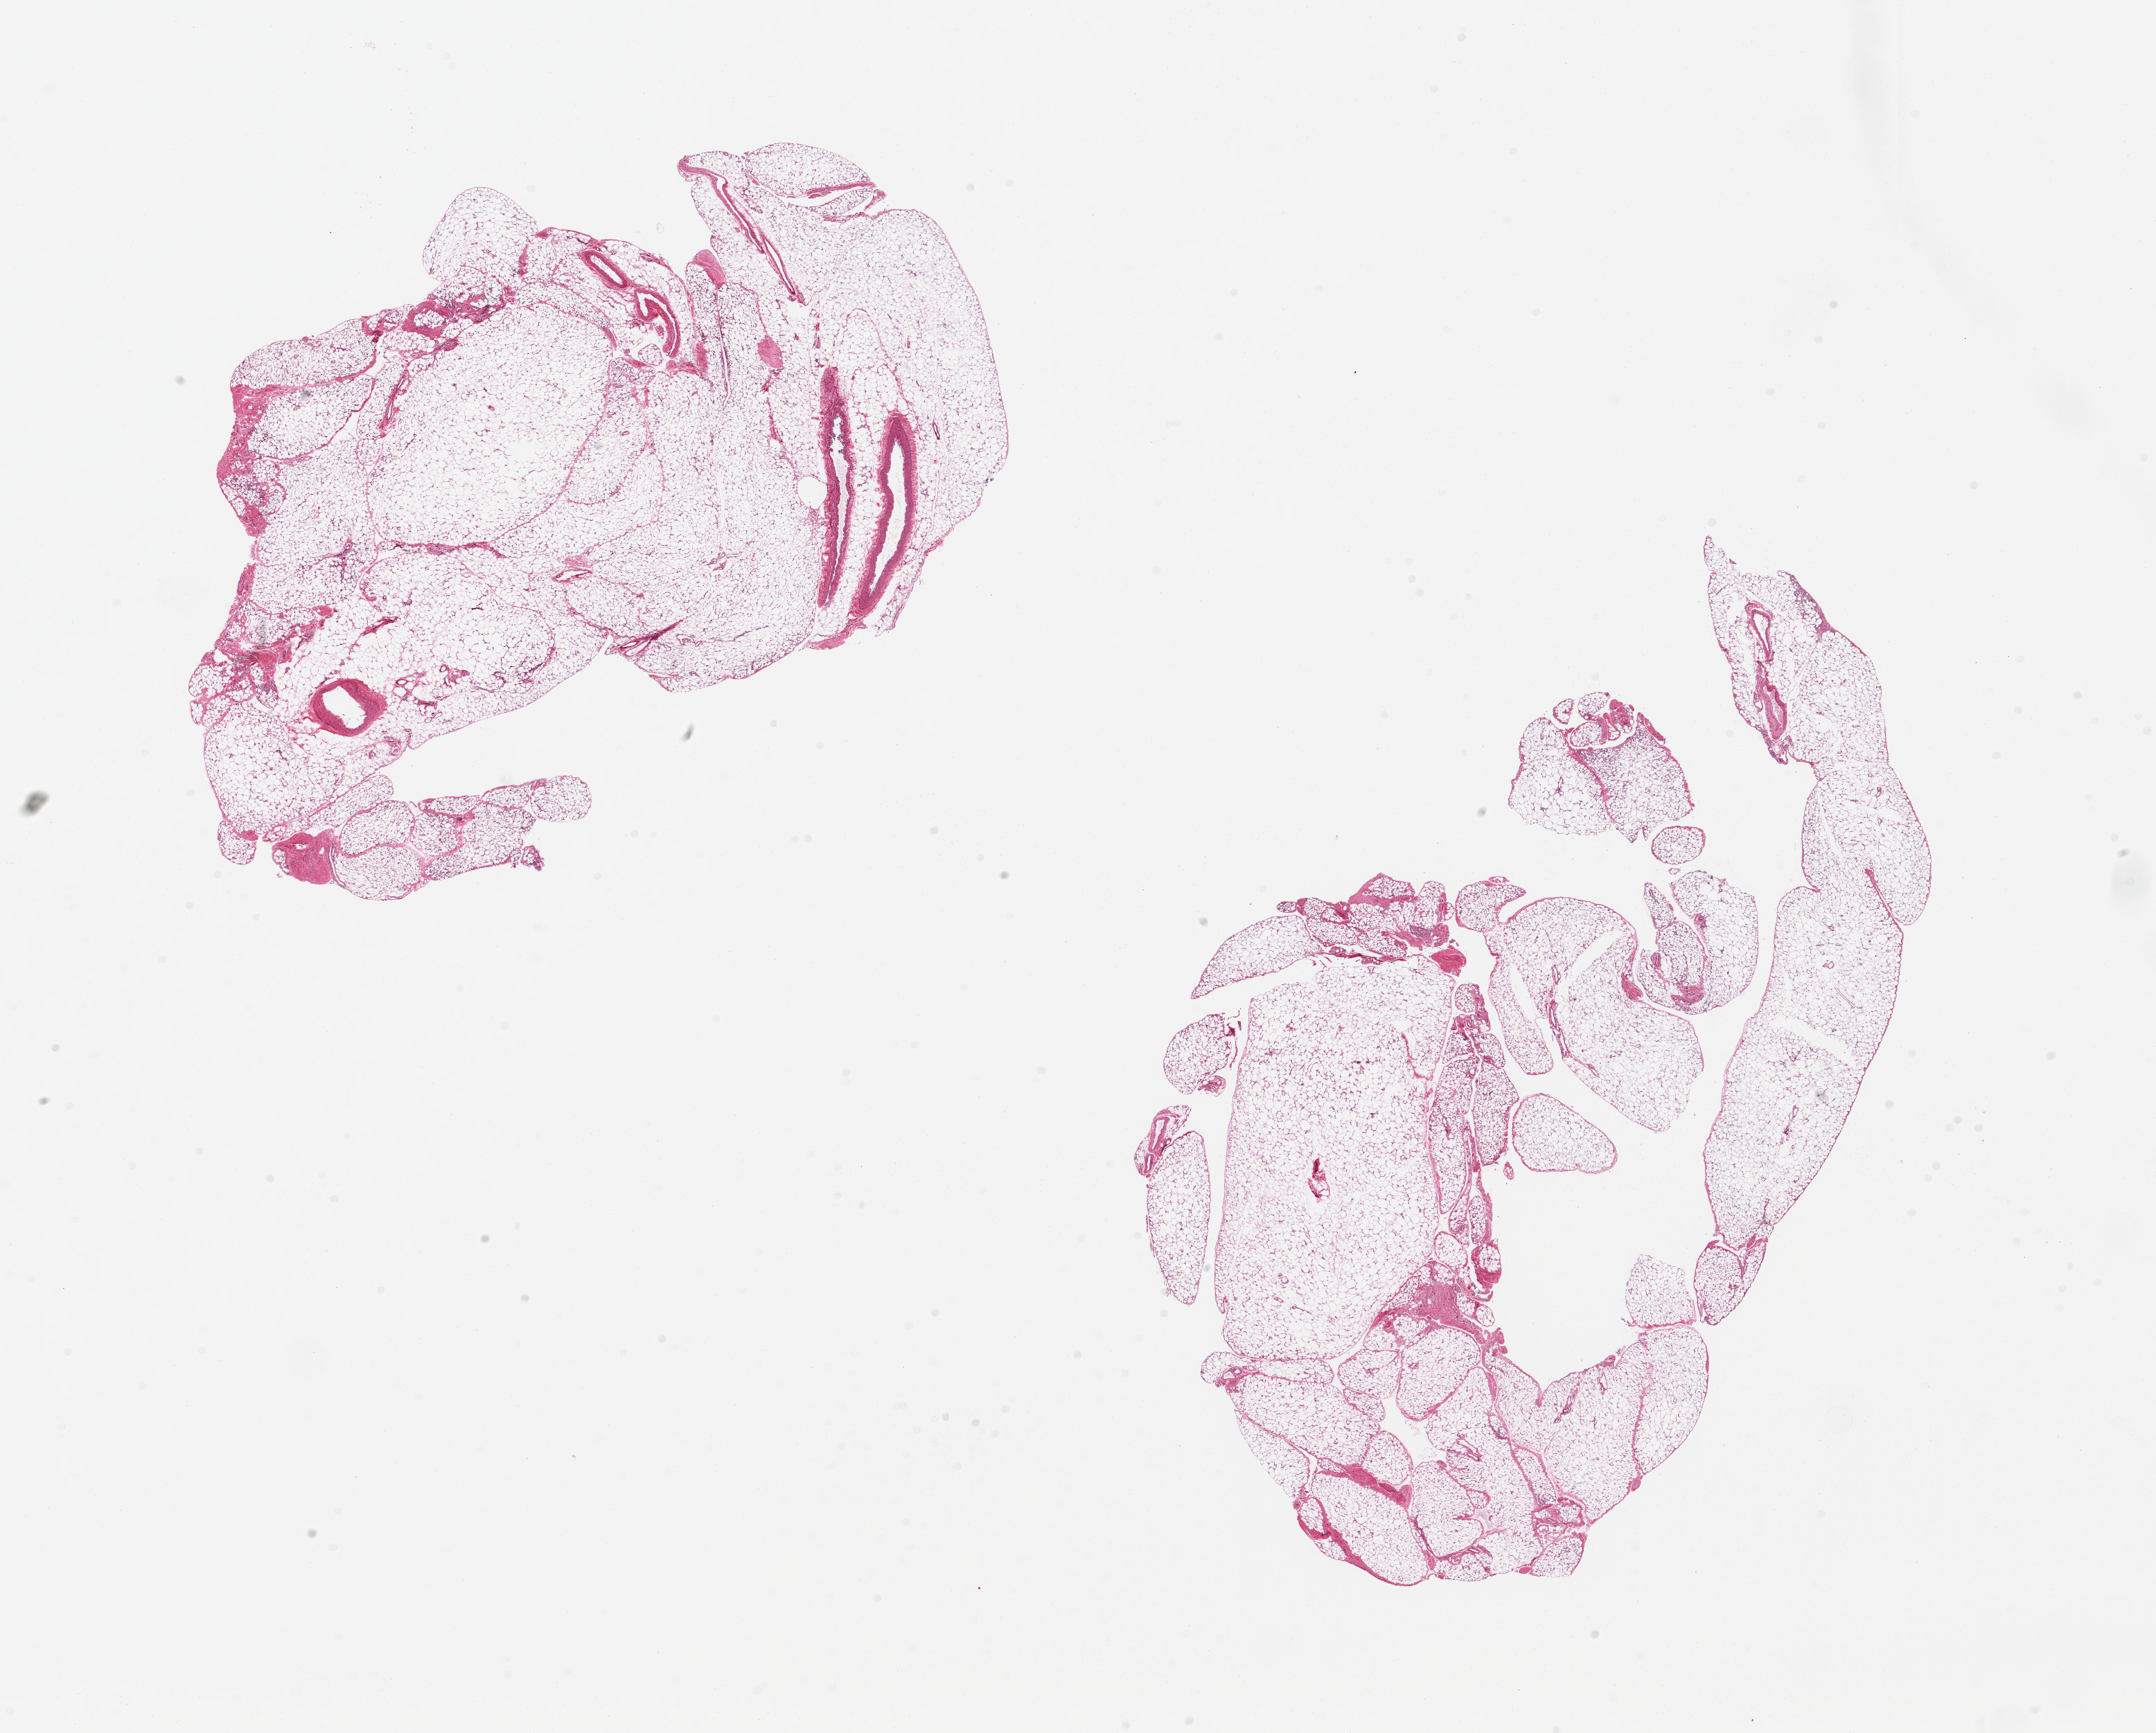
Digitized H&E-stained section, low-resolution overview of the scanned area, about 24.6 x 19.8 mm (acquisition: 20x scan). PAXgene-fixed paraffin-embedded (PFPE) section. Target tissue: omentum. Tissue donor sample. Donor: female.
Review note (as recorded): 2 pieces~10% interstitial vascular elements/fascia.